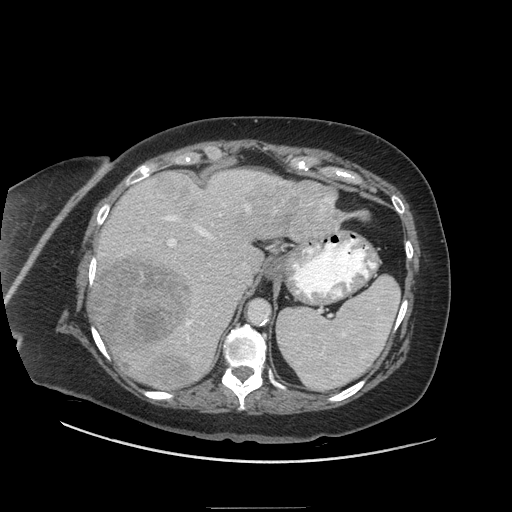
Contrast-enhanced abdominal CT (liver protocol), one axial slice; slice 43 of 81 in the series (ordered by position); 140 kVp; soft-tissue window (W 400 / L 40 HU); 512 × 512 image matrix, field of view 440 × 440 mm. From the clinical record (not read from this slice): diagnosis: hepatocellular carcinoma (patient treated with transarterial chemoembolisation; whether this scan precedes or follows treatment is not stated here); TNM stage (as recorded): Stage-II; Child-Pugh class: A.
Outlined on this slice (semi-automatically segmented with operator editing):
- liver parenchyma outside the tumour (the mass and vessels are separate outlines, so this box may not span the whole liver): bounding box [x1, y1, x2, y2] px = [88, 168, 338, 388]
- mass: [93, 172, 369, 391]
- liver vessels: [102, 173, 284, 358]